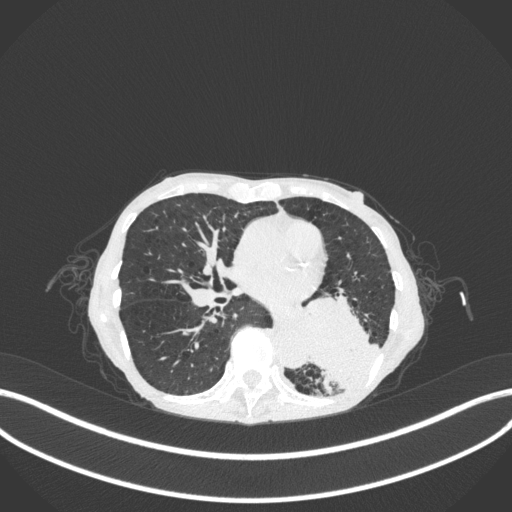
Chest CT, one axial slice; position 129 of 347 along the scan axis; reconstruction kernel B31f; 120 kVp; lung window (W 1500 / L -600 HU); 1 mm slice thickness; 512 × 512 image matrix. Patient: female, 70 years. From the clinical record (not read from this slice): clinical TNM (as recorded): T3 N0 M0; histopathological grade: G3.
Annotated regions visible in this slice (rectangle marked by the reading radiologist):
- lung tumour (recorded histology: small cell carcinoma): bounding box <287,285,389,388> (left, top, right, bottom; pixels)